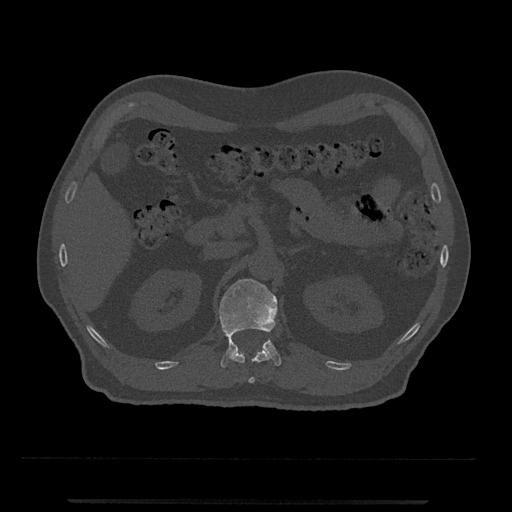
CT including the spine, one axial slice; position 364 of 797 along the scan axis; 120 kVp; bone window (W 1800 / L 400 HU); 0.5 mm slice thickness; 512 × 512 image matrix. Male patient, age 63 years. From the clinical record (not read from this slice): primary cancer: prostate.
Structures marked on this image (semi-automatically segmented with operator editing):
- L1 vertebra: bounding box (x1, y1, x2, y2) in pixels: (219, 278, 281, 368)
- T12 vertebra: (231, 348, 270, 383)